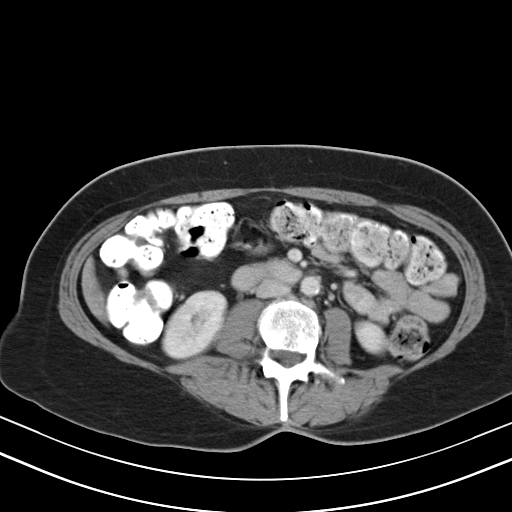
Contrast-enhanced abdominal CT, one axial slice; slice 13 of 47 in the series (ordered by position); reconstruction kernel B40s; soft-tissue window (W 400 / L 40 HU); 5 mm slice thickness; 512 × 512 image matrix, field of view 350 × 350 mm. Female patient. From the clinical record (not read from this slice): diagnosis: colorectal cancer liver metastases, imaged before liver resection; multiple liver metastases: no; largest metastasis: 3.5 cm; disease in both lobes: no.
Structures marked on this image (expert manual segmentation):
- liver: bounding box <94,293,99,306> (left, top, right, bottom; pixels)
- planned liver remnant (the part of the liver to remain after resection): <95,293,99,307>